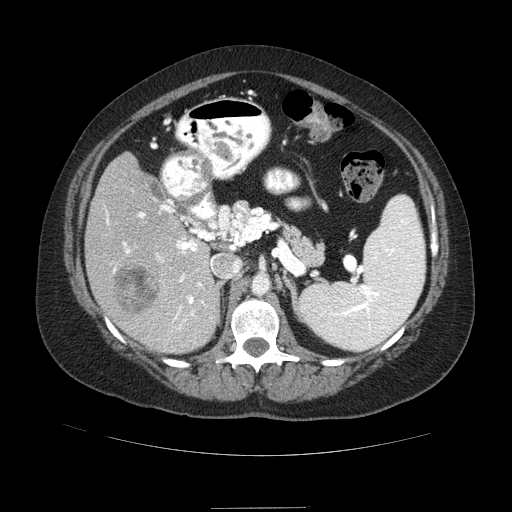
Contrast-enhanced abdominal CT (liver protocol), one axial slice; slice 45 of 89 in the series (ordered by position); reconstruction kernel STANDARD; soft-tissue window (W 400 / L 40 HU); 2.5 mm slice thickness; 512 × 512 image matrix, field of view 400 × 400 mm. Case-level facts recorded for this patient, not image findings: diagnosis: hepatocellular carcinoma (patient treated with transarterial chemoembolisation; whether this scan precedes or follows treatment is not stated here); TNM stage (as recorded): Stage-IIIB; Child-Pugh class: A; tumour nodularity: multinodular.
Outlined on this slice (semi-automatic segmentation, software-assisted and operator-edited):
- liver parenchyma outside the tumour (the mass and vessels are separate outlines, so this box may not span the whole liver): bounding box (x1, y1, x2, y2) in pixels: (84, 152, 220, 354)
- mass: (114, 261, 159, 314)
- liver vessels: (106, 205, 206, 330)